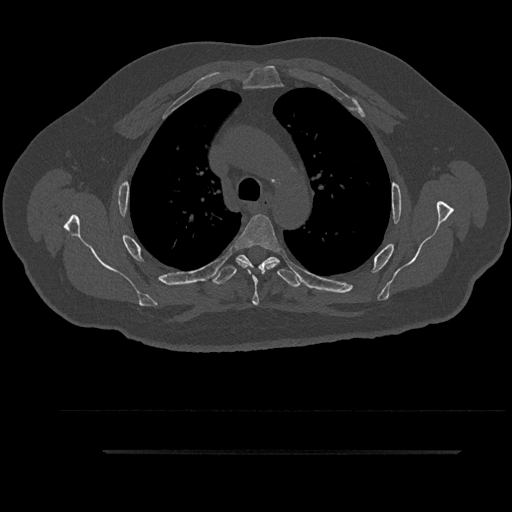
CT including the spine, one axial slice. Position 656 of 797 along the scan axis. 120 kVp. Bone window (W 1800 / L 400 HU). 0.5 mm slice thickness. 512 × 512 image matrix, field of view 432 × 432 mm. Patient: male, 63 years. From the clinical record (not read from this slice): primary cancer: renal.
Annotated regions visible in this slice (semi-automatically segmented with operator editing):
- T3 vertebra: bounding box [x1, y1, x2, y2] px = [236, 260, 298, 278]
- T4 vertebra: [235, 214, 280, 305]
- T5 vertebra: [213, 254, 301, 288]